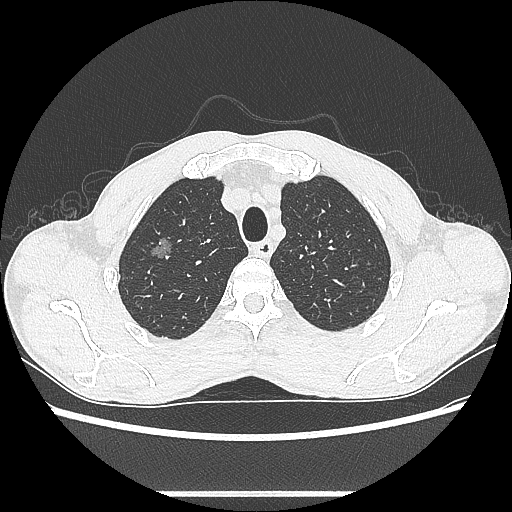
Chest CT, one axial slice. Position 495 of 601 along the scan axis. Reconstruction kernel LUNG. Lung window (W 1500 / L -600 HU). 0.62 mm slice thickness. 512 × 512 image matrix. Male patient, age 54 years. From the clinical record (not read from this slice): clinical TNM (as recorded): T1a N0 M0.
Structures marked on this image (rectangle marked by the reading radiologist):
- lung tumour (recorded histology: adenocarcinoma): box from (x=146, y=227) to (x=175, y=265) px